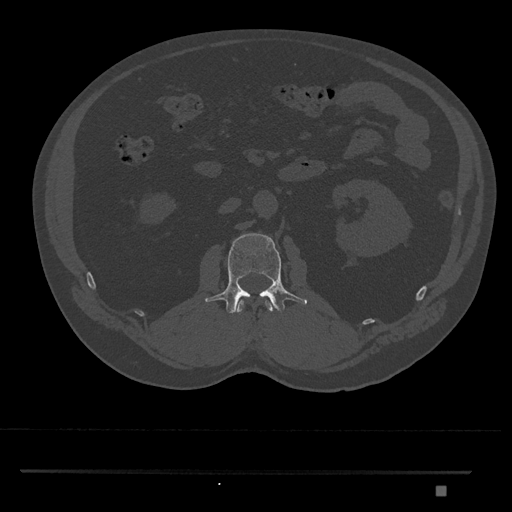
CT including the spine, one axial slice; slice 764 of 1134 in the series (ordered by position); reconstruction kernel Br40s/3; 120 kVp; bone window (W 1800 / L 400 HU); 0.5 mm slice thickness; 512 × 512 image matrix, field of view 429 × 429 mm. Male patient, age 65 years. Case-level facts recorded for this patient, not image findings: primary cancer: prostate.
Structures marked on this image (semi-automatic segmentation, software-assisted and operator-edited):
- L1 vertebra: bounding box (x1, y1, x2, y2) in pixels: (235, 300, 274, 314)
- L2 vertebra: (205, 233, 307, 314)